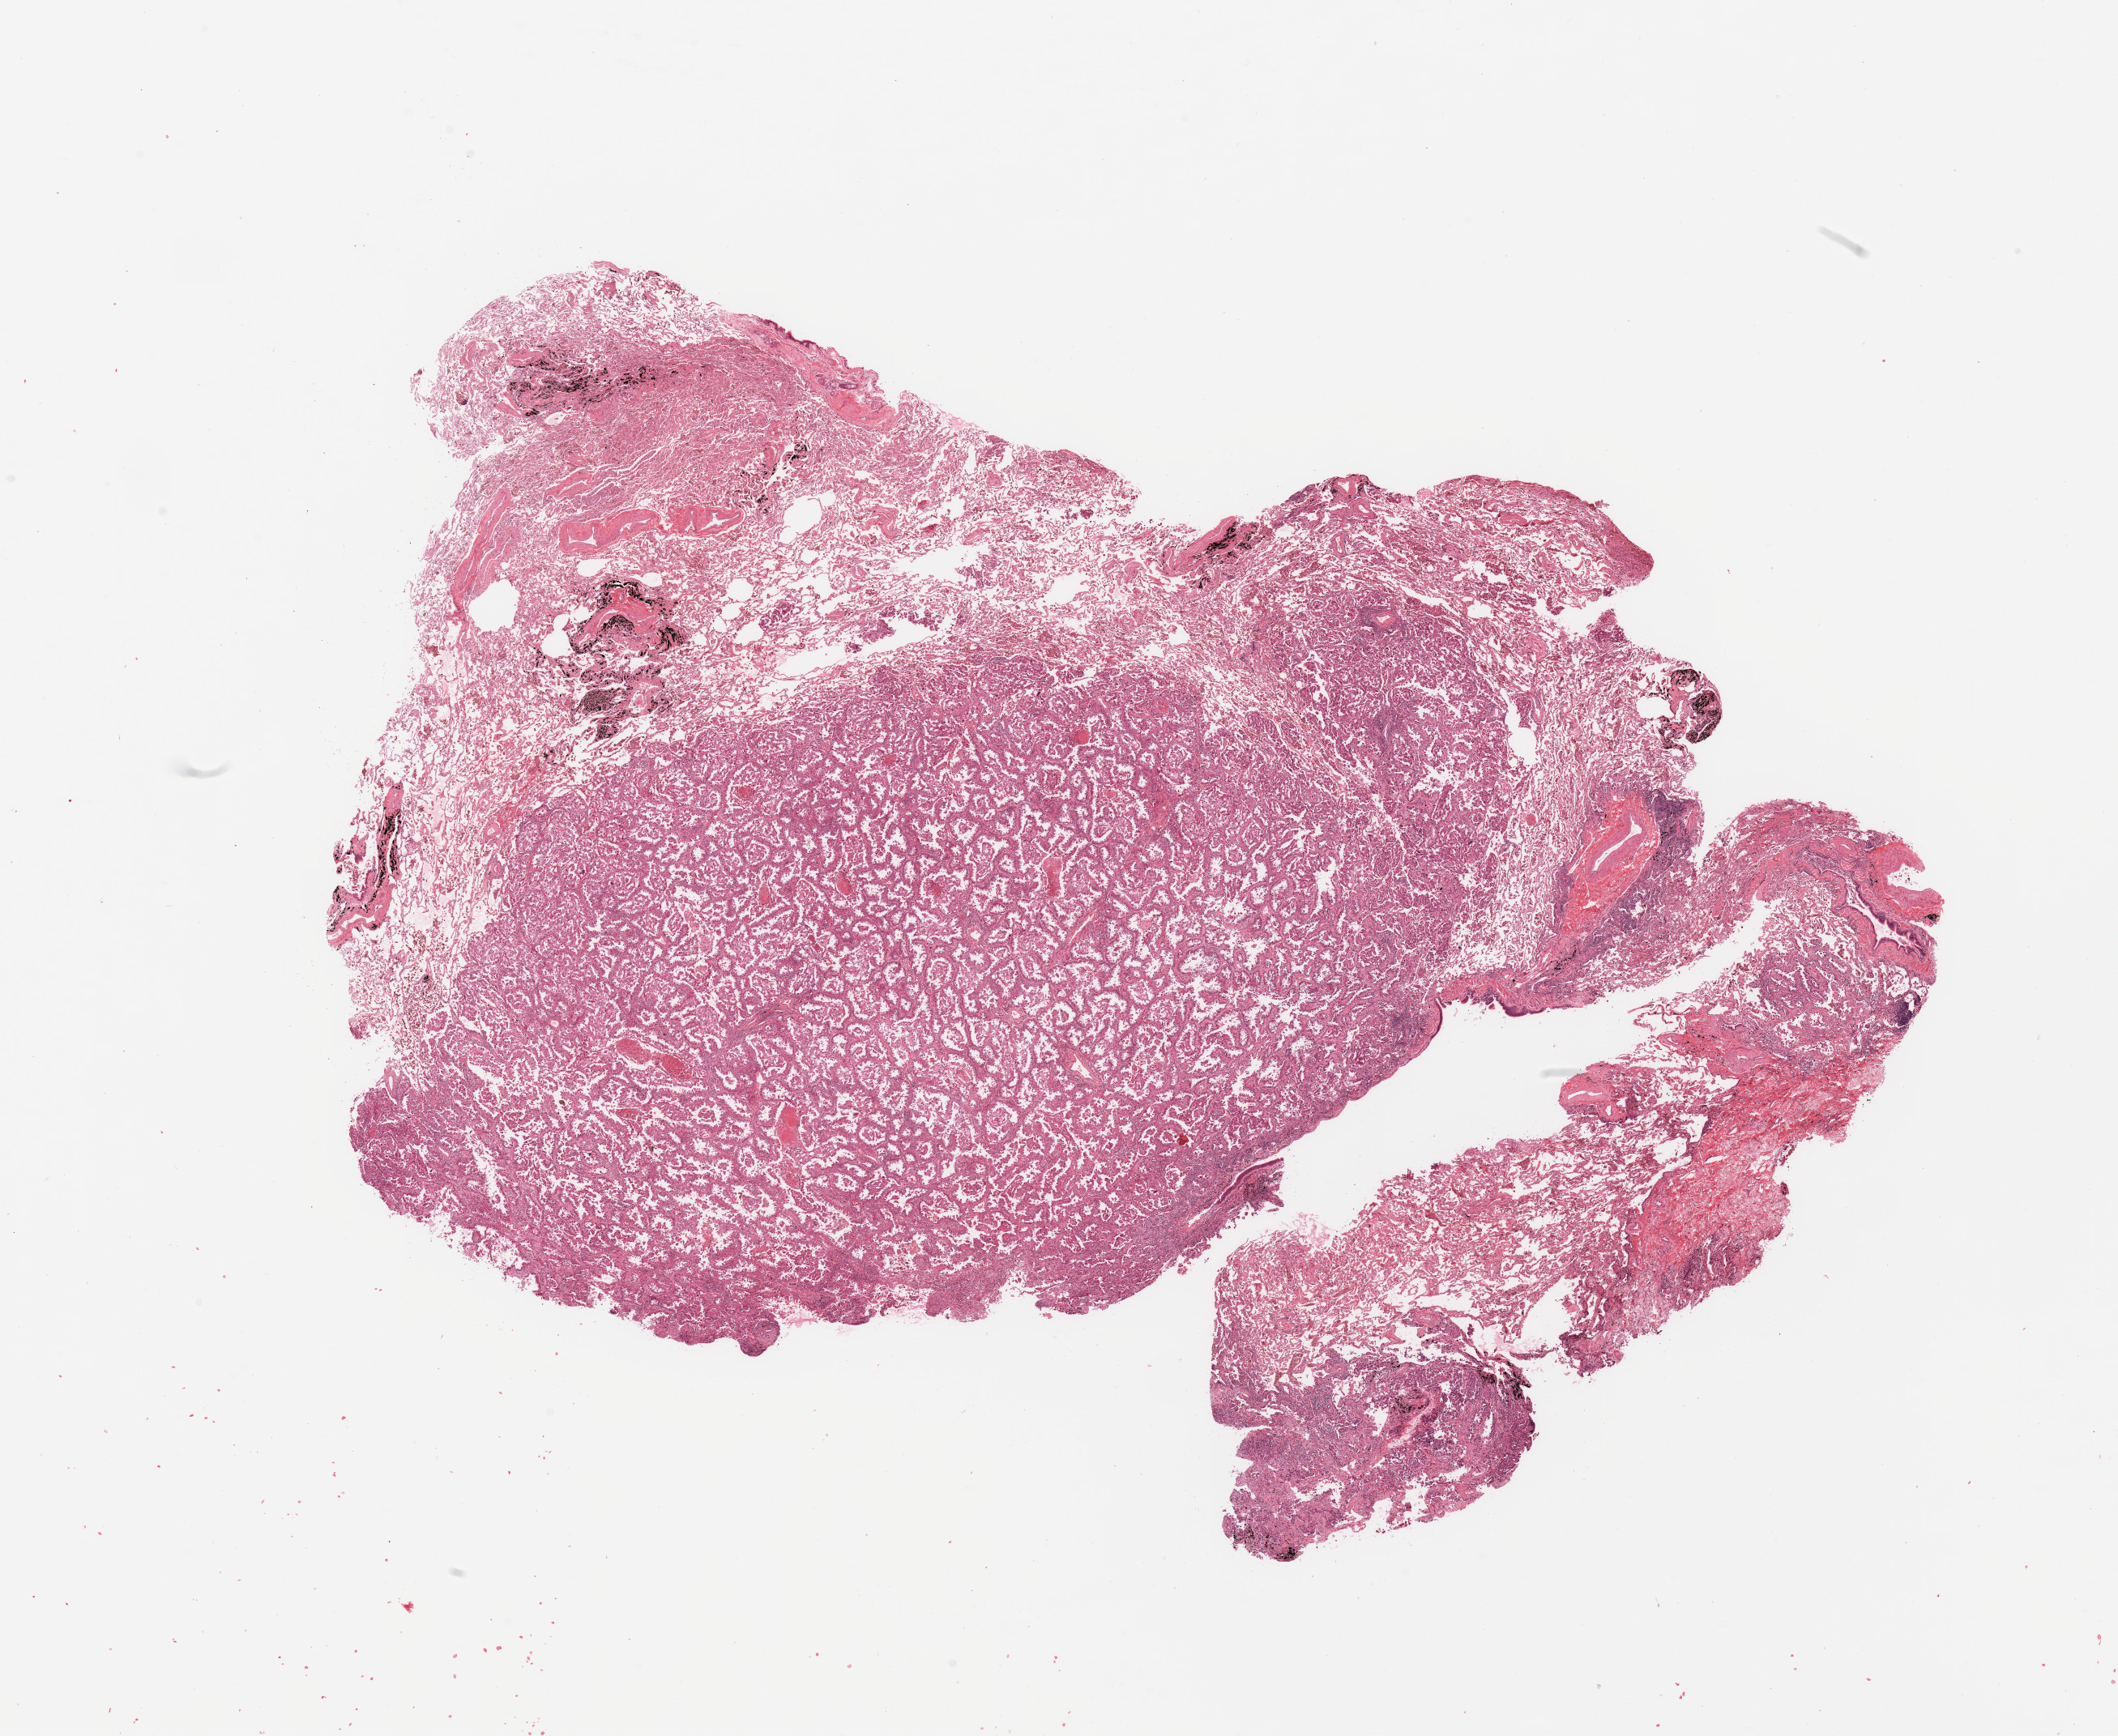
Digitized H&E tissue section (whole slide) — shown as a low-resolution overview of the whole scanned area (about 20.7 x 16.9 mm). Tumour tissue sample, lung. Patient: male, age 59 years. Histologic grade: G2 (moderately differentiated).
* primary tumour site (as recorded): right upper lobe
* AJCC pathologic stage: IIIA
* diagnosis: Adenocarcinoma, NOS